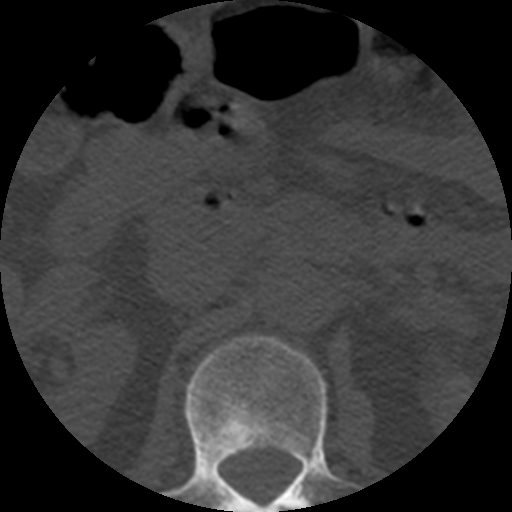
CT including the spine, one axial slice; slice 182 of 508 in the series (ordered by position); reconstruction kernel STANDARD; 120 kVp; bone window (W 1800 / L 400 HU); 1.25 mm slice thickness; 512 × 512 image matrix, field of view 160 × 160 mm. Patient age 57 years. Case-level facts recorded for this patient, not image findings: primary cancer: prostate.
Structures marked on this image (semi-automatically segmented with operator editing):
- L1 vertebra: bounding box <163,335,360,512> (left, top, right, bottom; pixels)